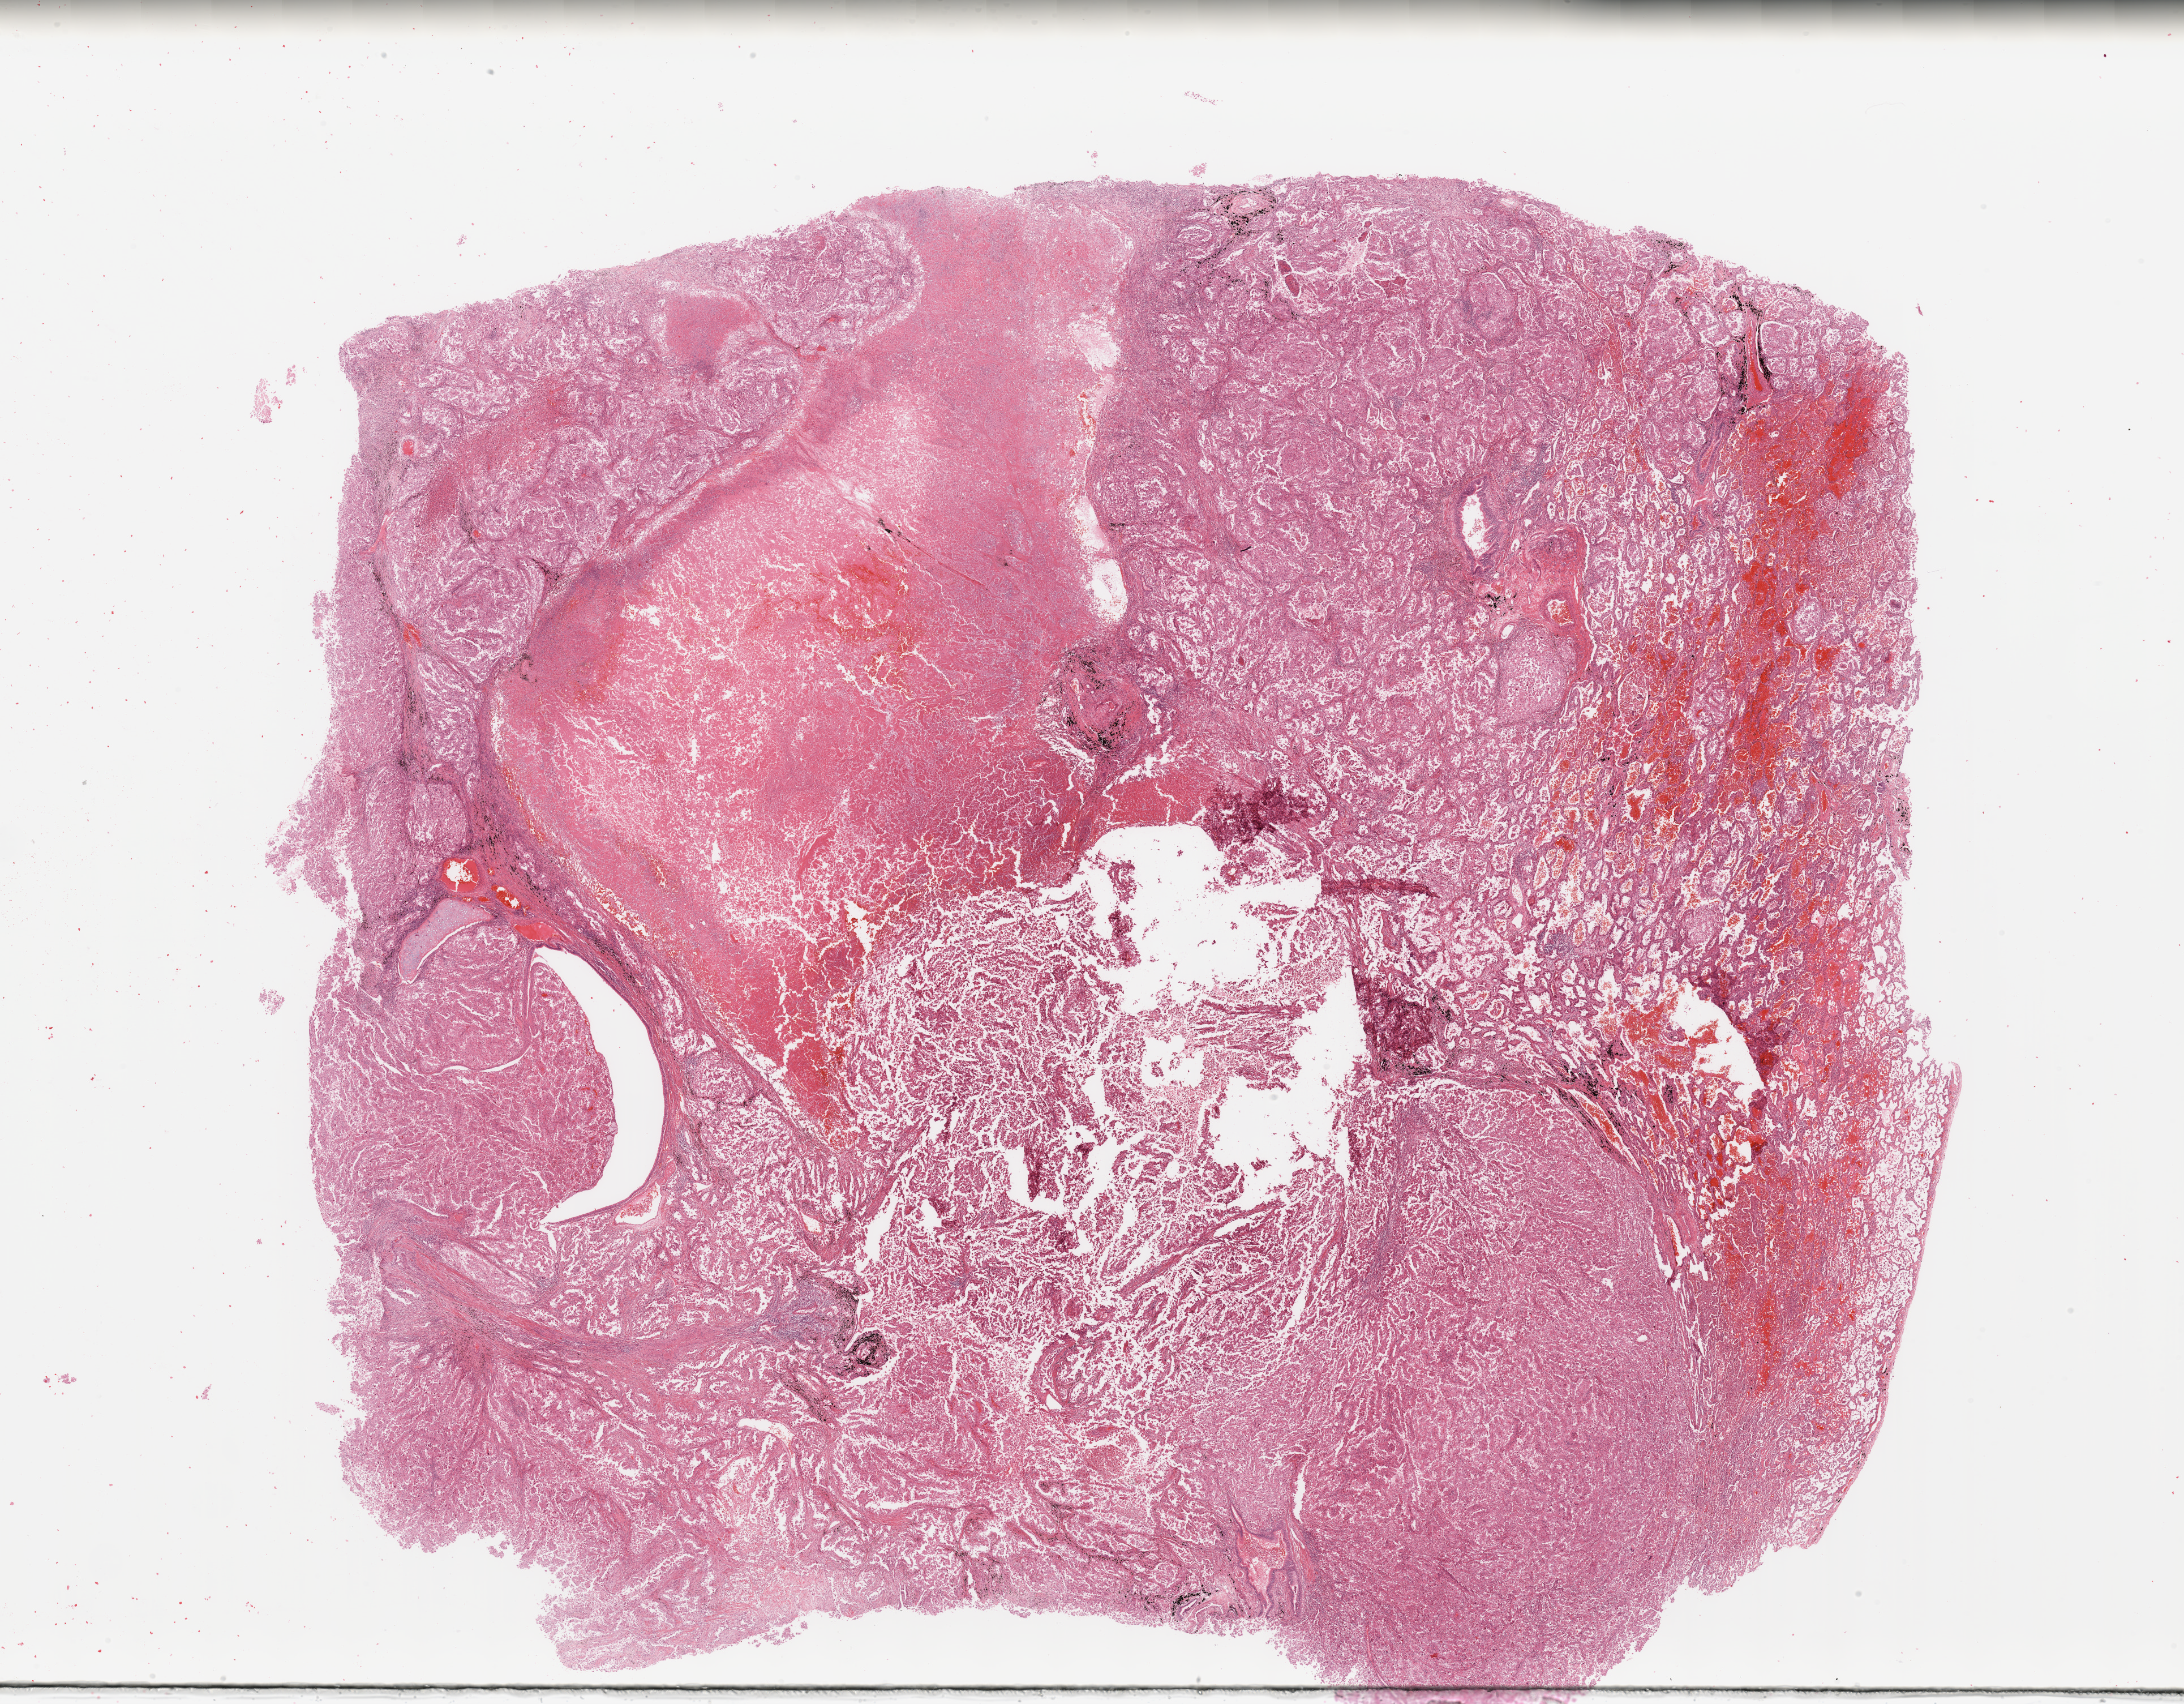
Whole-slide histology image, H&E, low-resolution overview of the scanned area, about 30.5 x 23.8 mm; lung, tumour tissue. 55-year-old male patient. Histologic grade: G2 (moderately differentiated).
Histologic diagnosis: Adenocarcinoma, NOS. AJCC pathologic stage: IIIA.